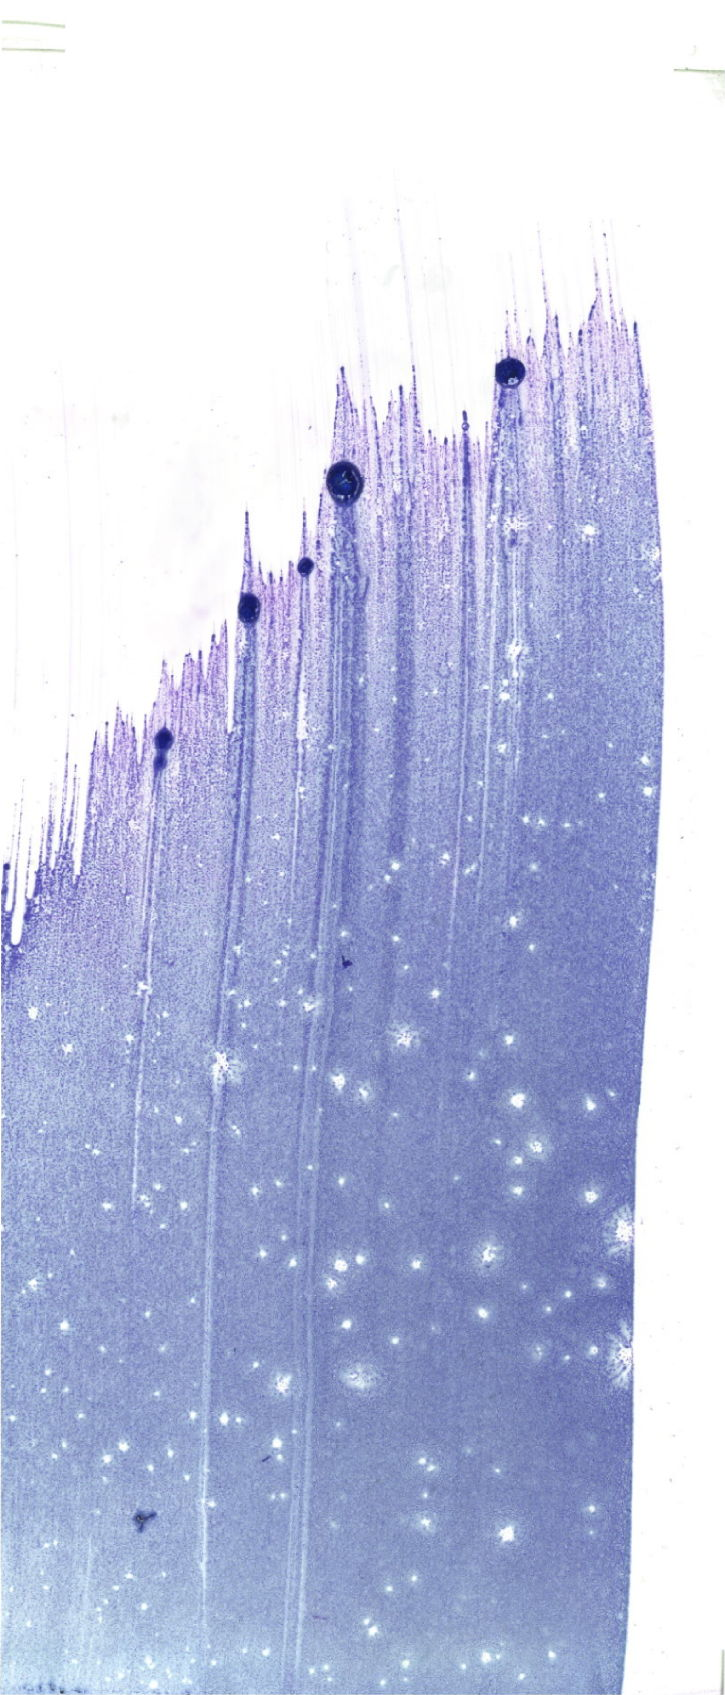
Bone marrow aspirate smear, May-Grünwald-Giemsa (MGG) stain, whole-slide image — low-resolution overview of the scanned area, about 20.6 x 48.0 mm. Patient sex: male.
Diagnosis: Acute Megakaryoblastic Leukemia.